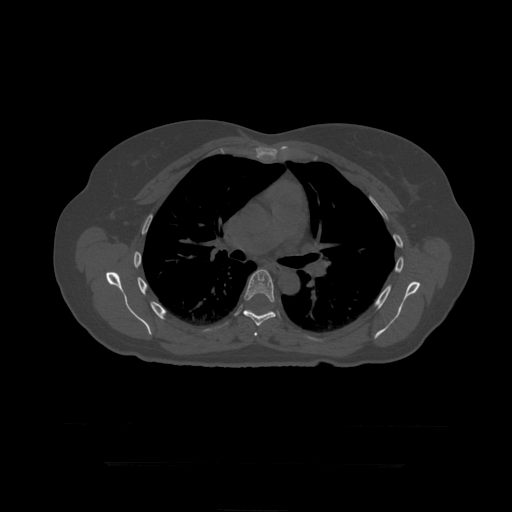
CT including the spine, one axial slice. Slice 300 of 399 in the series (ordered by position). Reconstruction kernel STANDARD. Bone window (W 1800 / L 400 HU). 1.25 mm slice thickness. 512 × 512 image matrix, field of view 450 × 450 mm. Patient age 41 years. From the clinical record (not read from this slice): primary cancer: breast.
Annotated regions visible in this slice (semi-automatically segmented with operator editing):
- T6 vertebra: bounding box (x1, y1, x2, y2) in pixels: (254, 332, 258, 336)
- T7 vertebra: (243, 270, 276, 326)